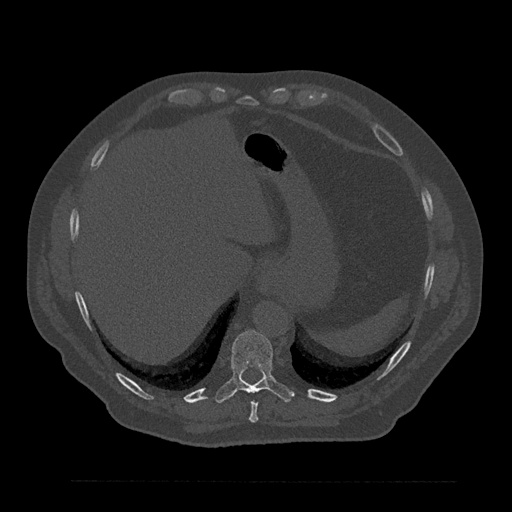
CT including the spine, one axial slice; slice 360 of 797 in the series (ordered by position); reconstruction kernel Br40s/3; bone window (W 1800 / L 400 HU); 0.5 mm slice thickness; 512 × 512 image matrix, field of view 430 × 430 mm. Male patient, age 61 years. Case-level facts recorded for this patient, not image findings: primary cancer: prostate.
Outlined on this slice (semi-automatically segmented with operator editing):
- T10 vertebra: box from (x=215, y=330) to (x=294, y=403) px
- T9 vertebra: (x=249, y=401)–(x=258, y=423)